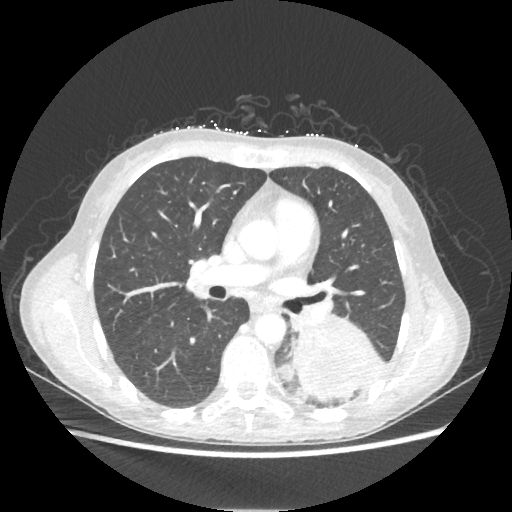
Chest CT, one axial slice; slice 120 of 221 in the series (ordered by position); reconstruction kernel STANDARD; lung window (W 1500 / L -600 HU); 1.25 mm slice thickness; 512 × 512 image matrix. Female patient, age 53 years. From the clinical record (not read from this slice): clinical TNM (as recorded): T3 N0 M0.
Annotated regions visible in this slice (bounding box drawn by a radiologist):
- lung tumour (recorded histology: adenocarcinoma): bounding box <291,317,384,401> (left, top, right, bottom; pixels)